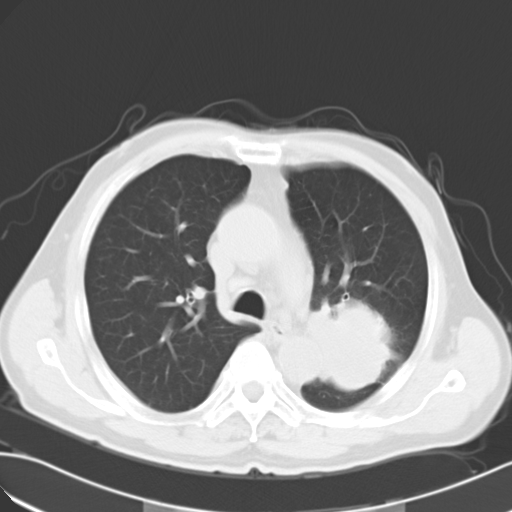
Chest CT, one axial slice. Reconstruction kernel B40f. Lung window (W 1500 / L -600 HU). 10 mm slice thickness. 512 × 512 image matrix. Patient: male, 63 years. From the clinical record (not read from this slice): clinical TNM (as recorded): T3 N3 M1a.
Outlined on this slice (rectangle marked by the reading radiologist):
- lung tumour (recorded histology: large cell carcinoma): bounding box (x1, y1, x2, y2) in pixels: (305, 296, 389, 403)